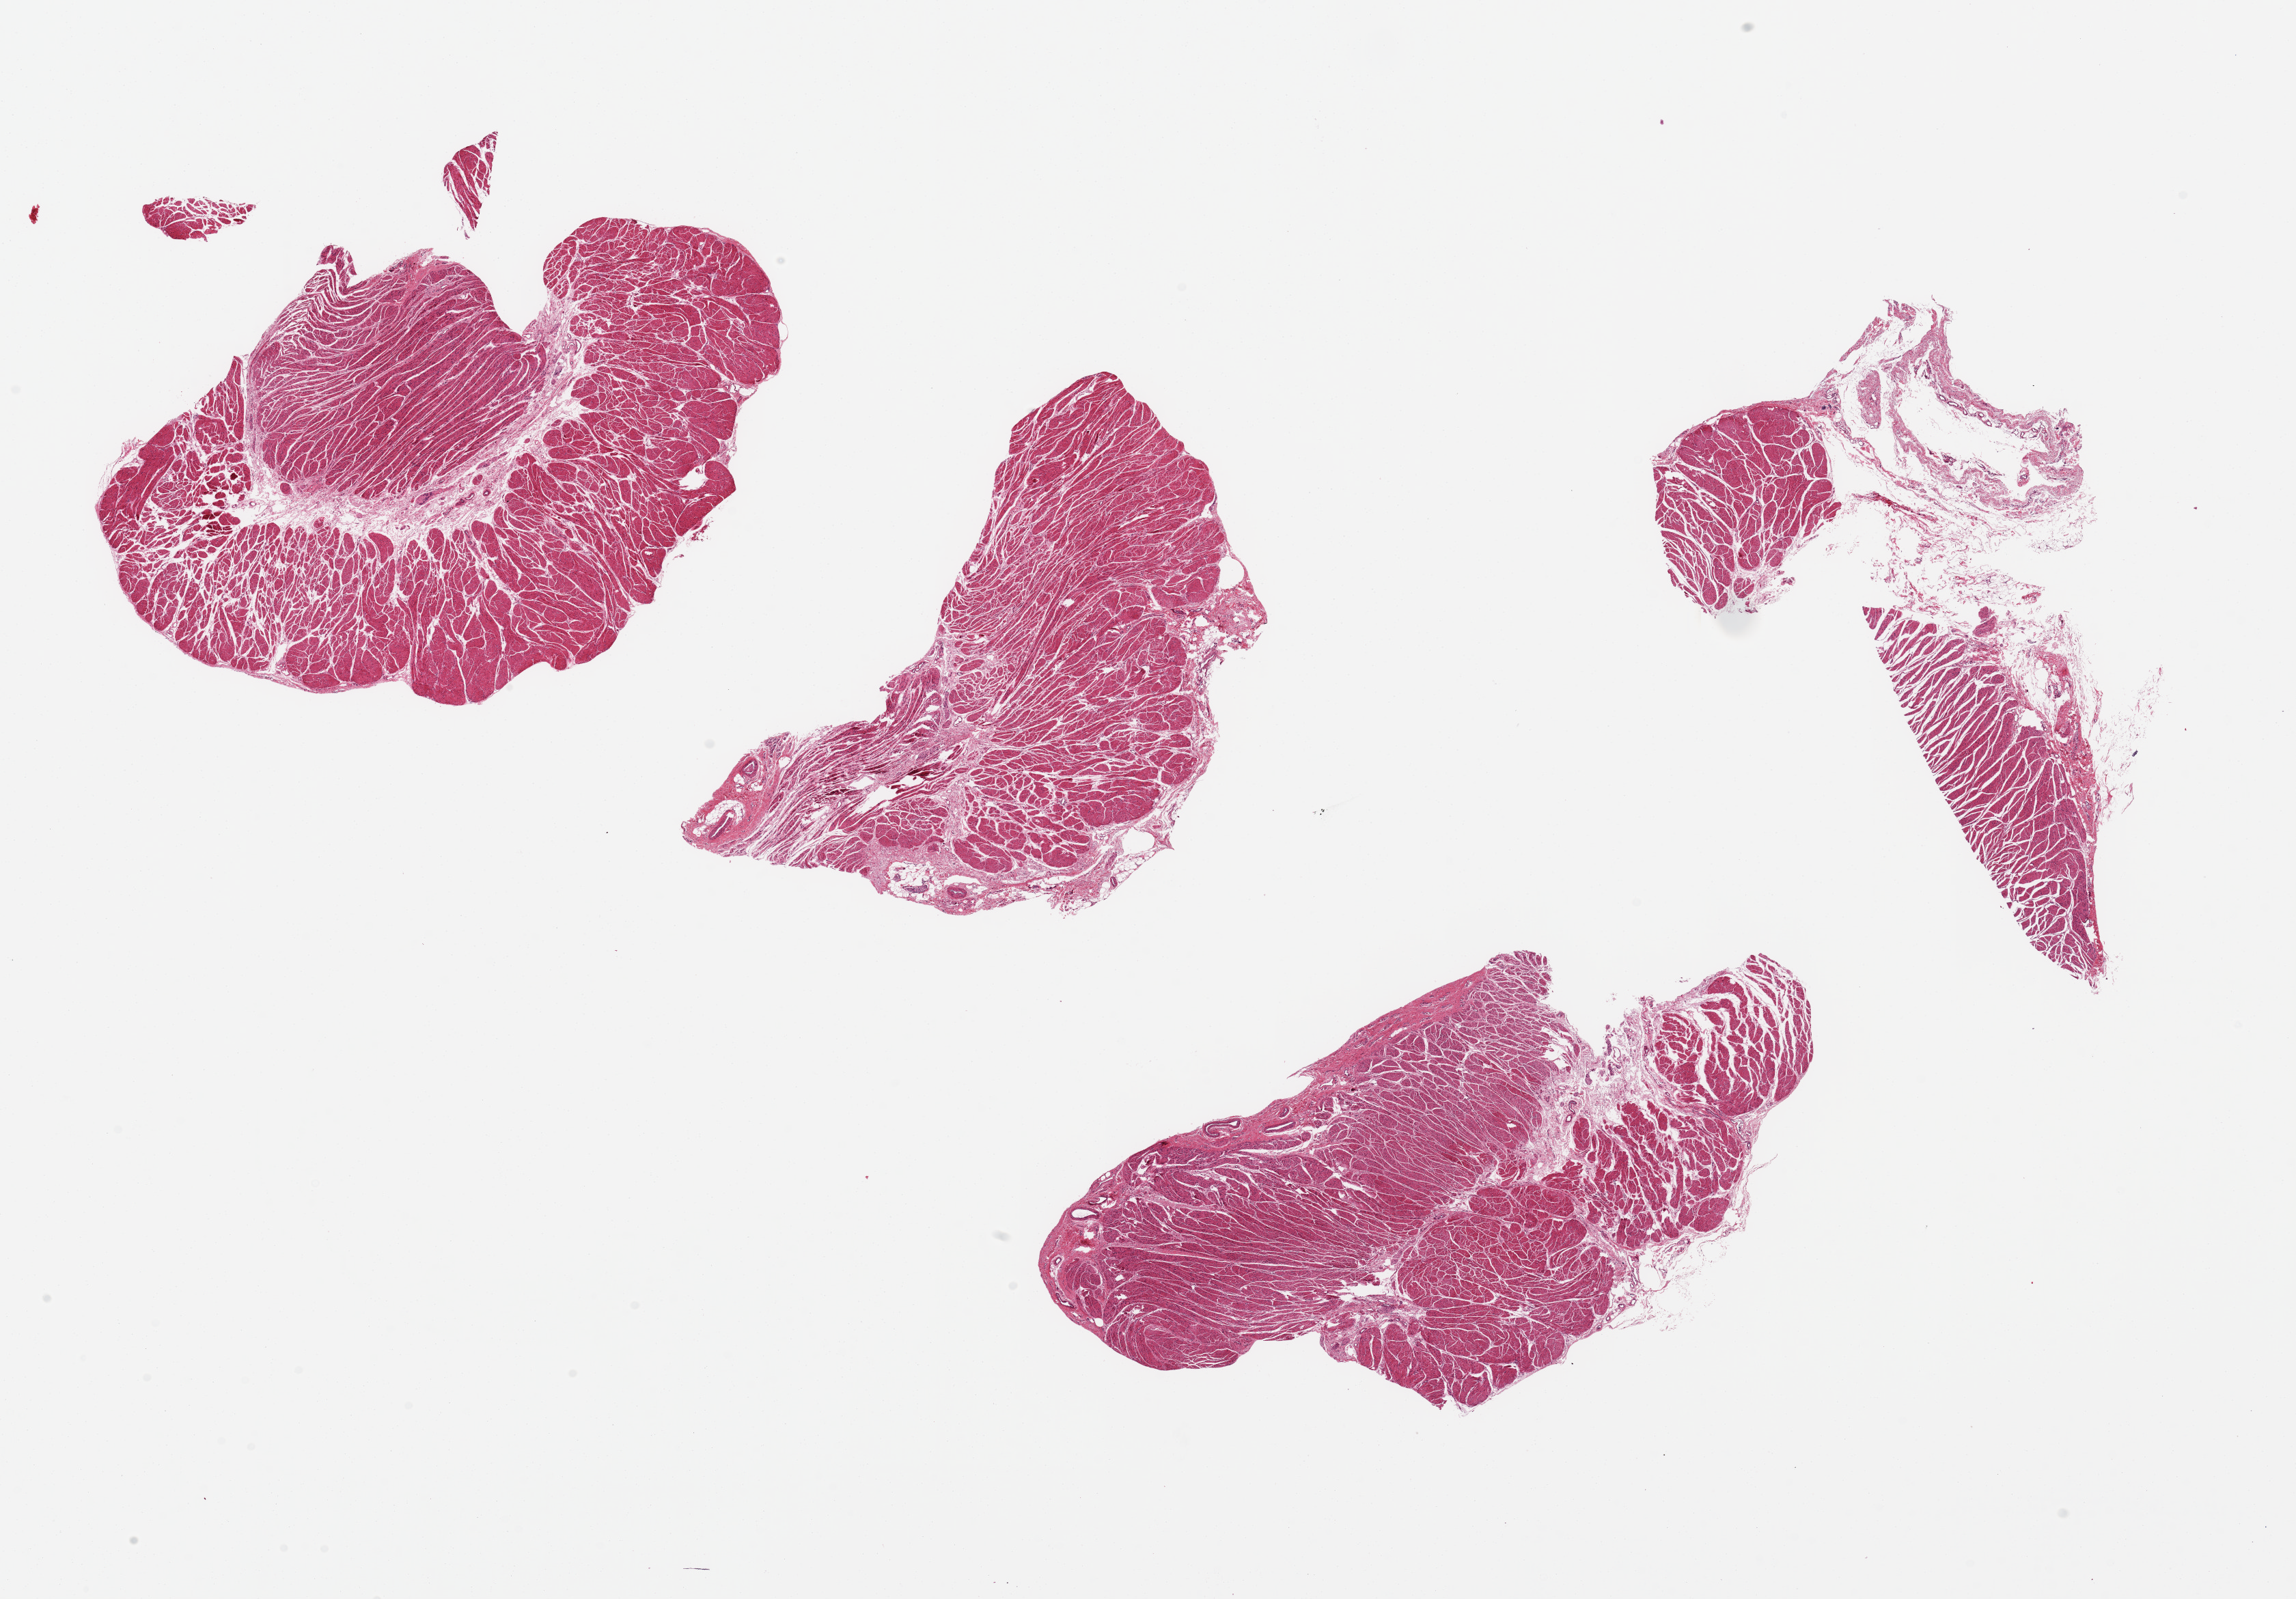
Whole-slide image, hematoxylin and eosin (H&E) stain, a low-resolution overview of the entire scanned area, about 26.6 x 18.5 mm. PAXgene-fixed, paraffin-embedded tissue. Sampled site (target tissue): esophageal muscle. Tissue donor sample. Male donor.
Pathologist's review note for this sample: 4 ~8x4.5mm pieces.